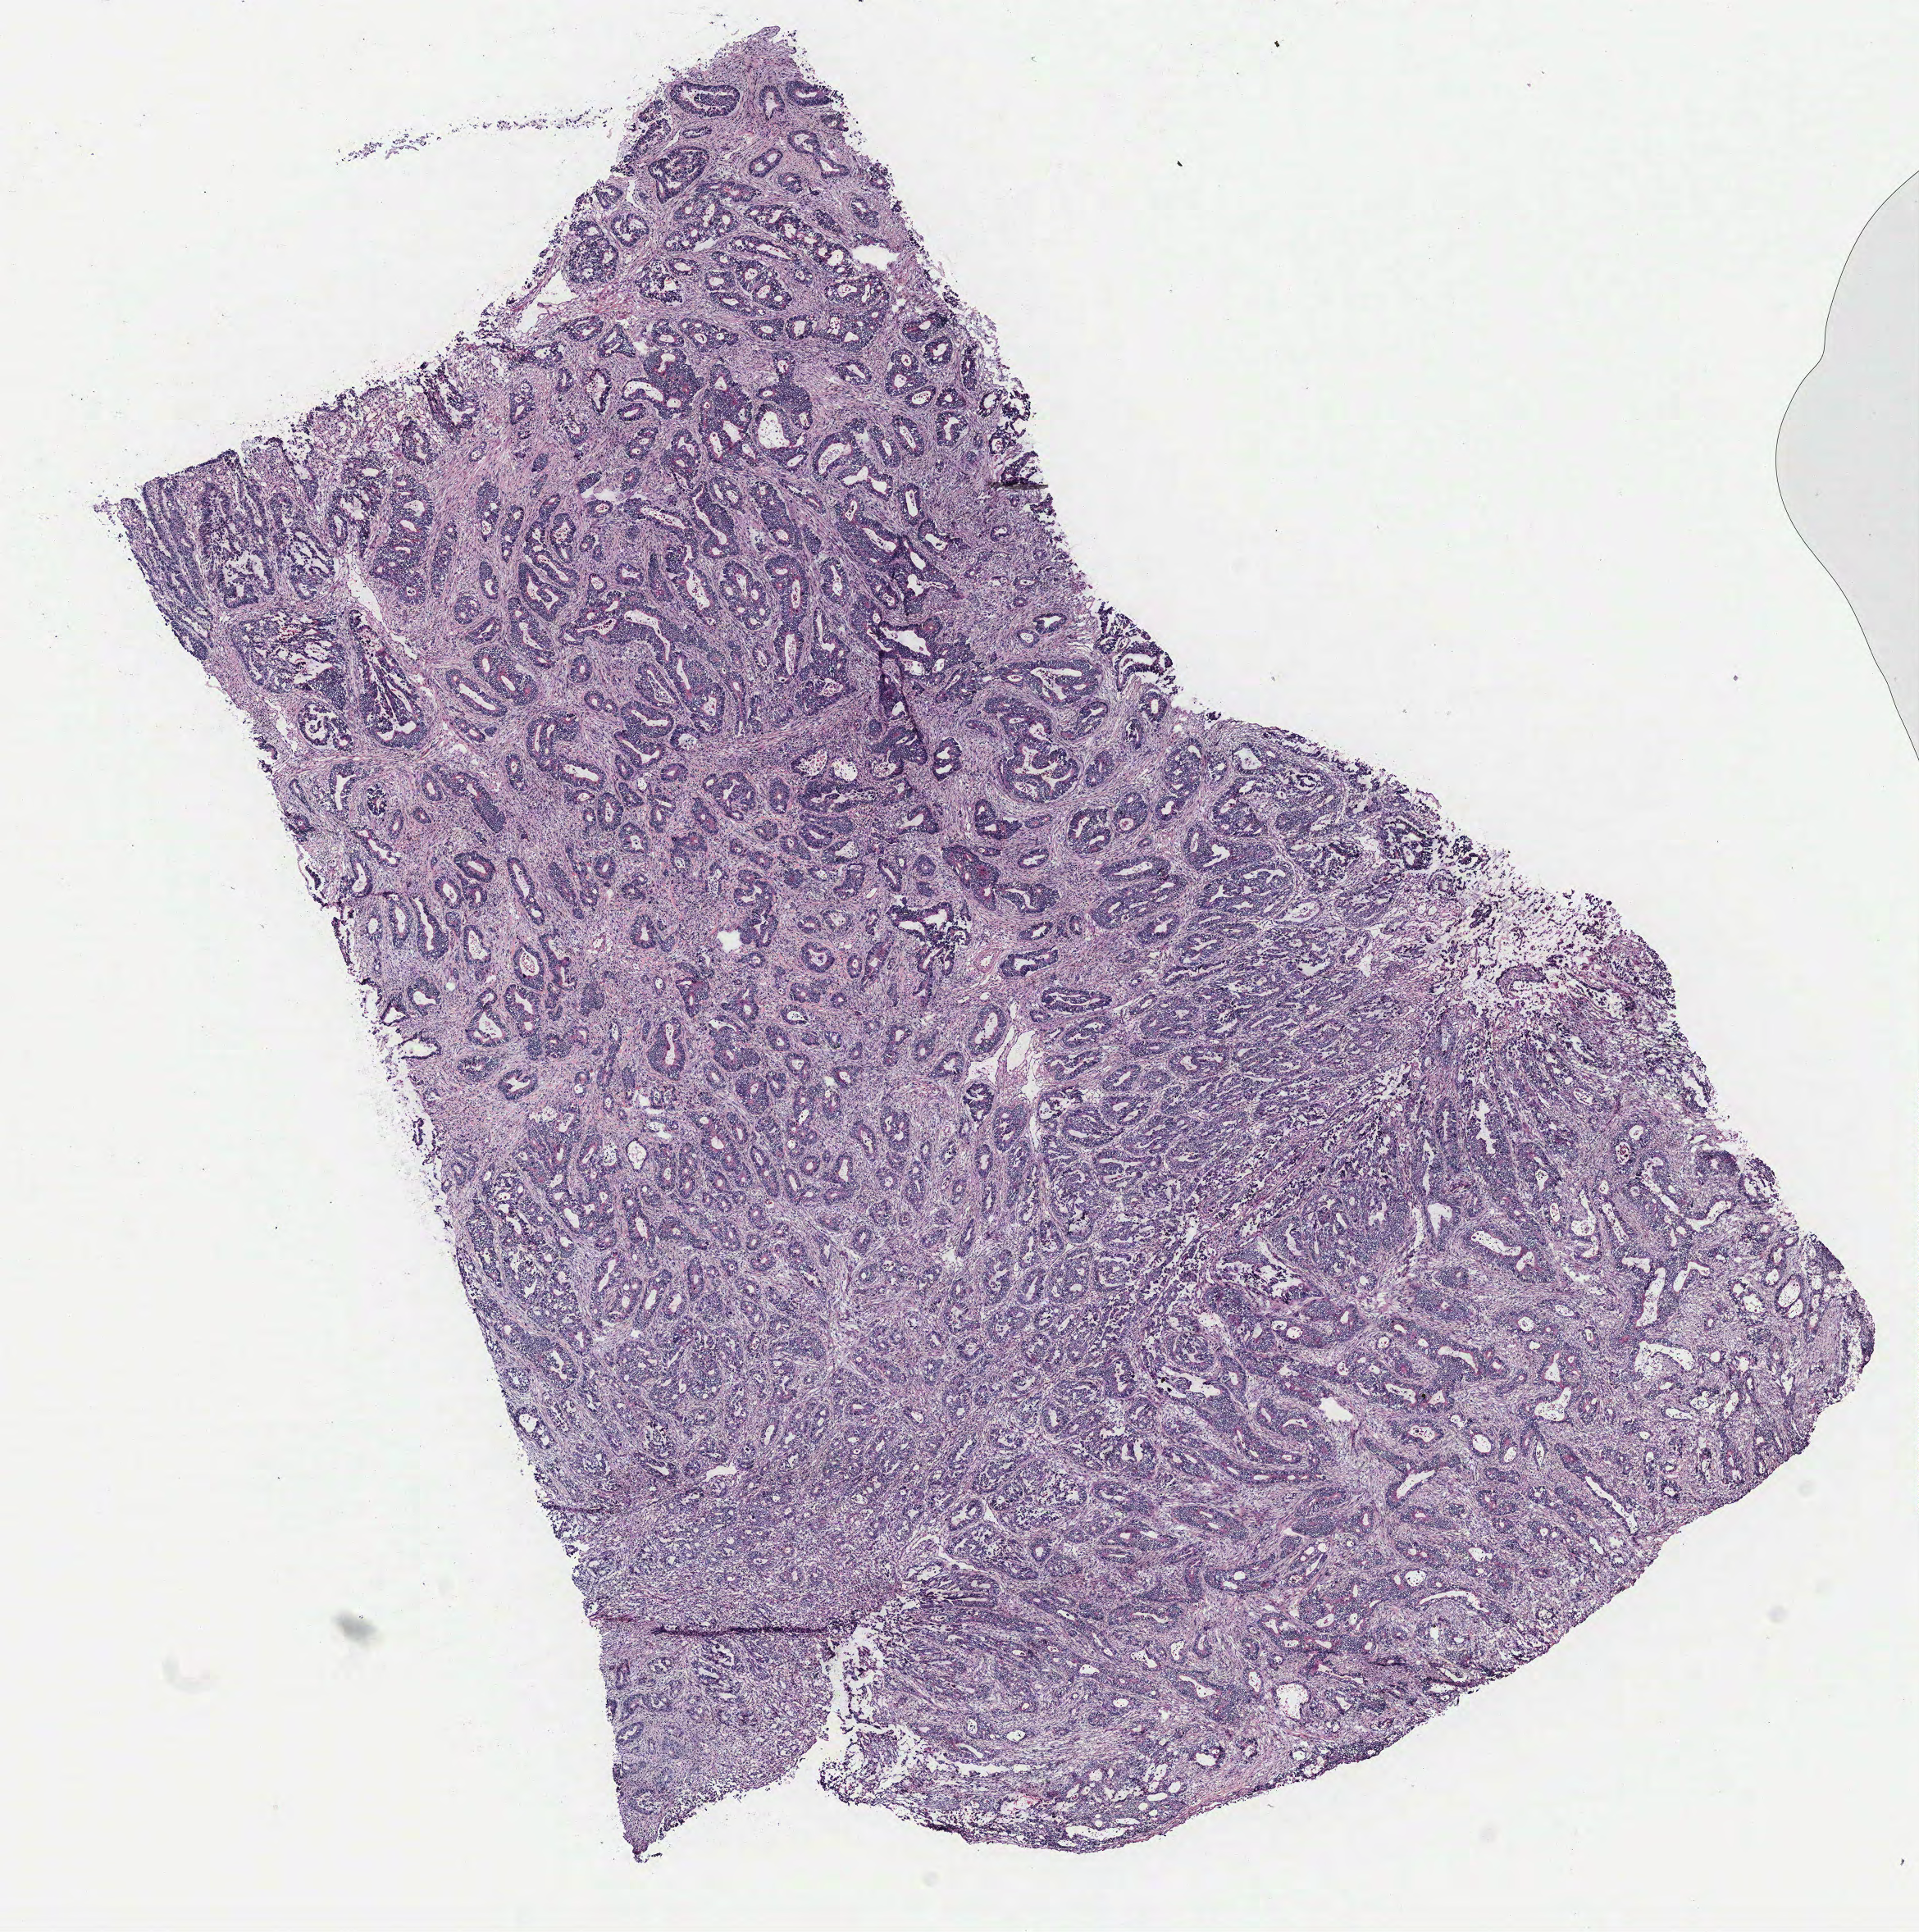
H&E-stained whole-slide image — whole scanned area (about 9.4 x 9.4 mm, slide scanned at 40x) shown as a low-resolution overview. Colon, tissue type not recorded. Patient sex: female.
Patient diagnosis: Adenocarcinoma, NOS.